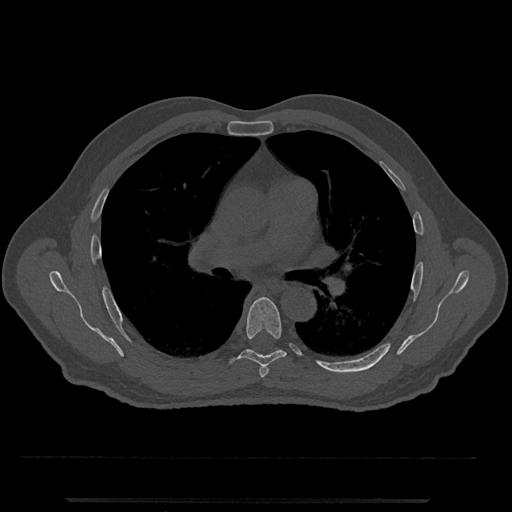
CT including the spine, one axial slice; reconstruction kernel Br40s/3; 120 kVp; bone window (W 1800 / L 400 HU); 0.5 mm slice thickness; 512 × 512 image matrix, field of view 419 × 419 mm. Patient: male, 63 years. Case-level facts recorded for this patient, not image findings: primary cancer: prostate.
Outlined on this slice (semi-automatic segmentation, software-assisted and operator-edited):
- T5 vertebra: bounding box [x1, y1, x2, y2] px = [259, 364, 269, 378]
- T6 vertebra: [231, 297, 286, 367]